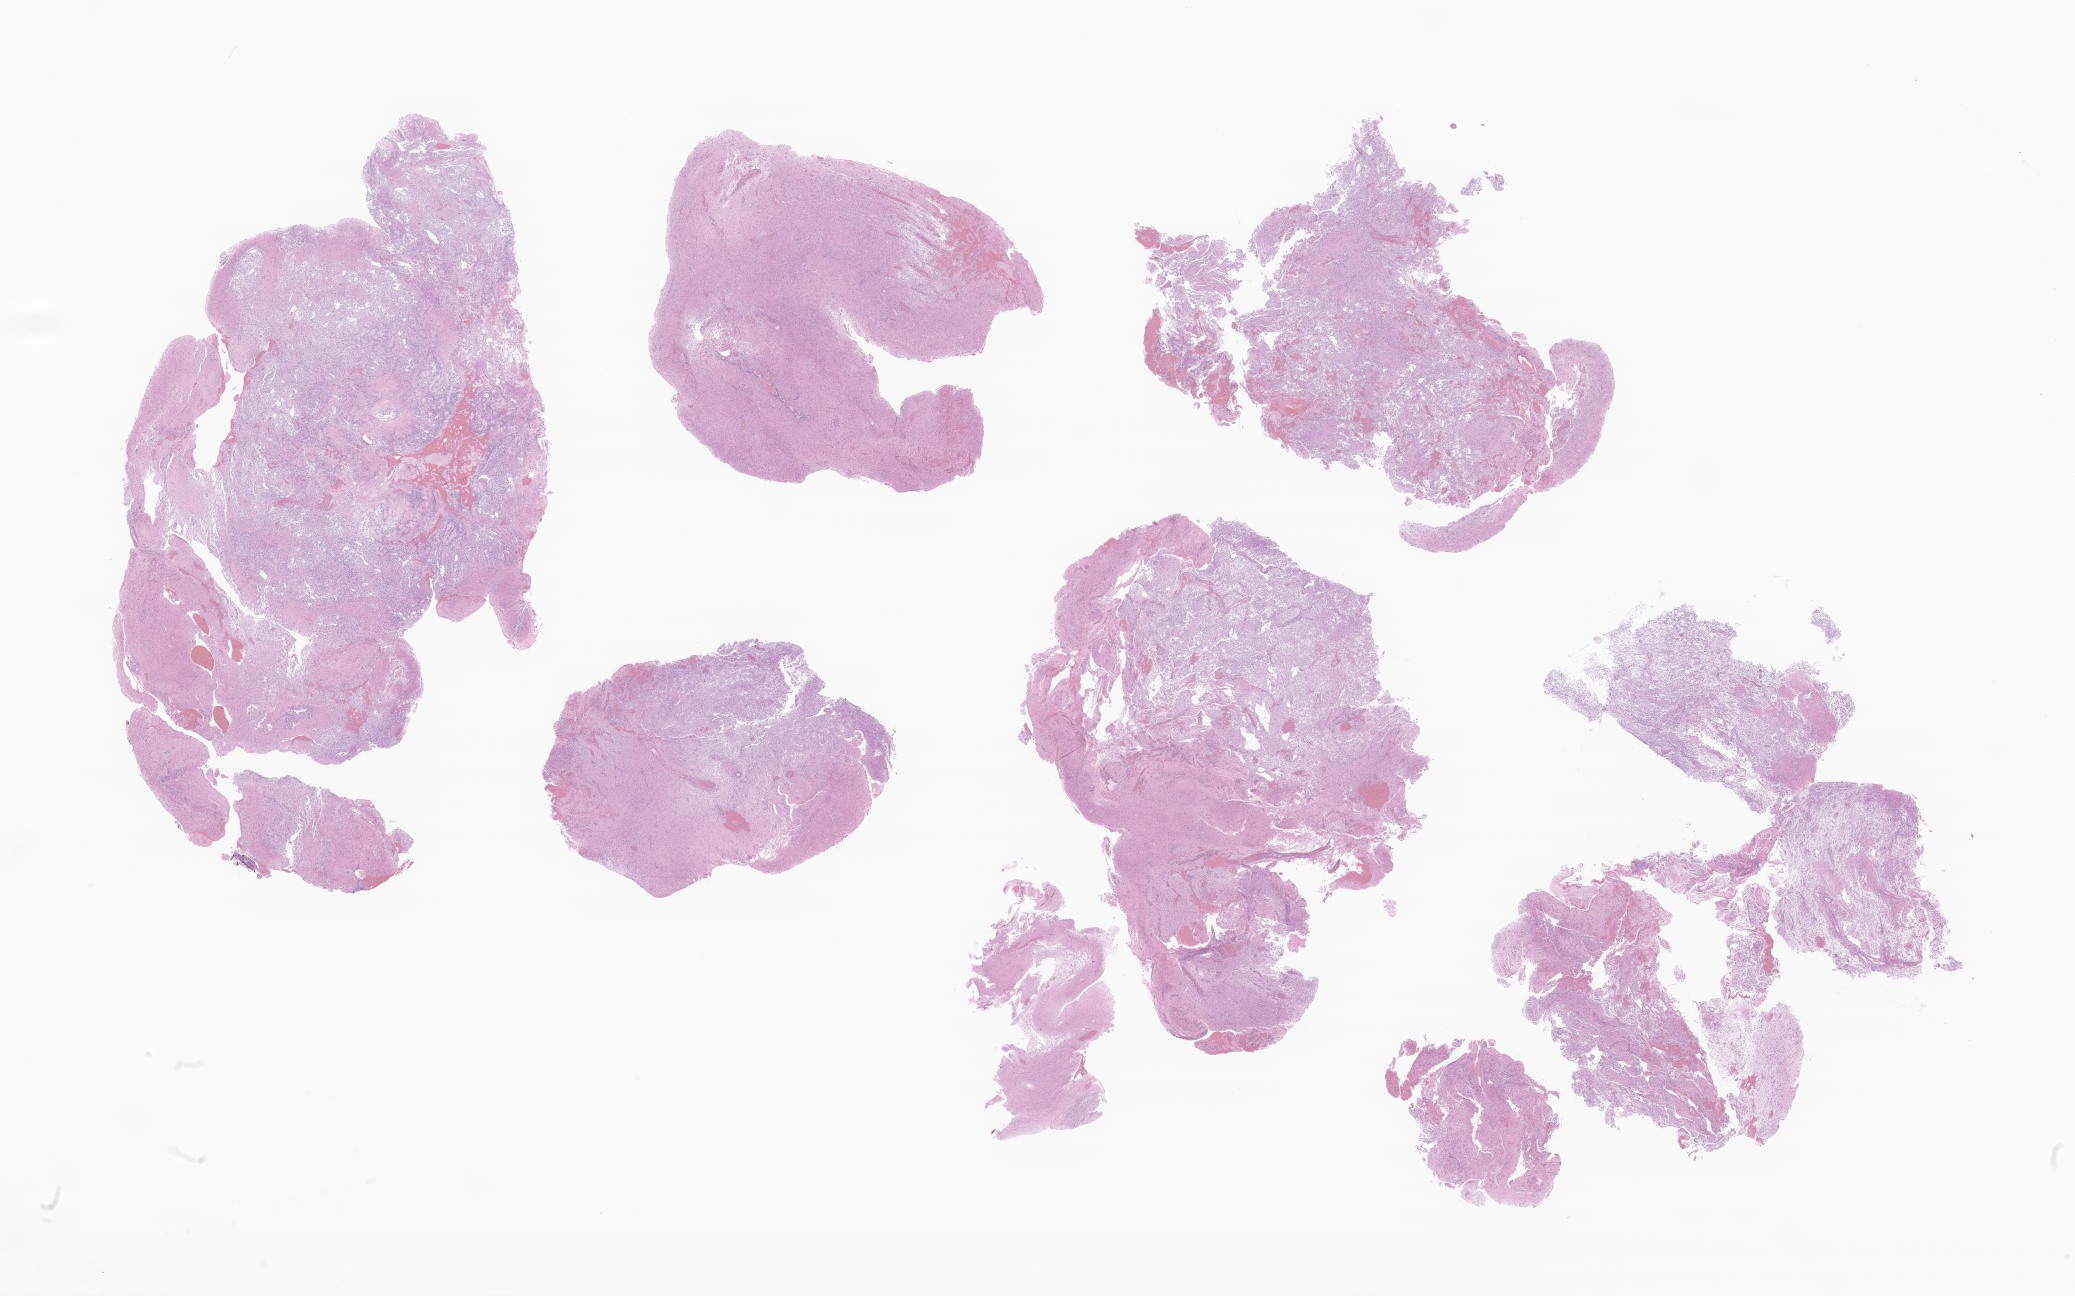
Whole-slide image, H&E stain of tumor tissue from the cerebellum — whole scanned area (about 35.0 x 21.9 mm) shown as a low-resolution overview; FFPE section. Patient: male, age 133 months (11 years 1 month).
Diagnosis: Pilocytic astrocytoma.